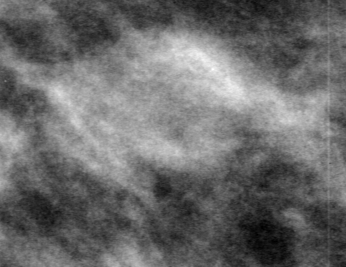
Crop from a digitized film mammogram around one marked abnormality, left breast, MLO view.
- Marked abnormality: mass, shape oval, margins obscured; BI-RADS assessment category 3; subtlety rating 4 on a 1 (subtle) to 5 (obvious) scale; pathology (as recorded): malignant.